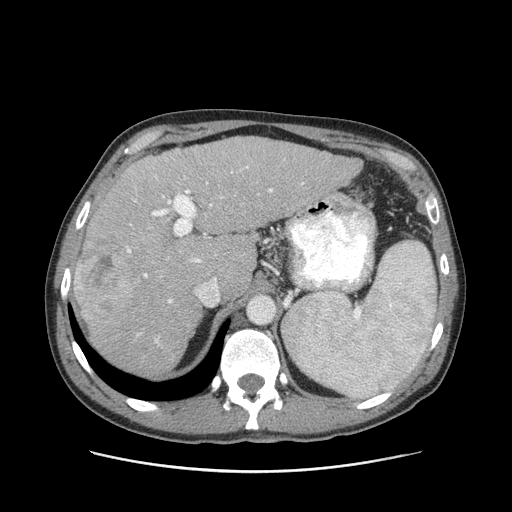
Contrast-enhanced abdominal CT (liver protocol), one axial slice. Slice 67 of 93 in the series (ordered by position). Soft-tissue window (W 400 / L 40 HU). 2.5 mm slice thickness. 512 × 512 image matrix. Case-level facts recorded for this patient, not image findings: diagnosis: hepatocellular carcinoma (patient treated with transarterial chemoembolisation; whether this scan precedes or follows treatment is not stated here); TNM stage (as recorded): Stage-II; Child-Pugh class: A; tumour differentiation: moderately differentiated; tumour nodularity: multinodular.
Annotated regions visible in this slice (semi-automatically segmented with operator editing):
- liver parenchyma outside the tumour (the mass and vessels are separate outlines, so this box may not span the whole liver): bounding box (x1, y1, x2, y2) in pixels: (72, 136, 360, 376)
- mass: (76, 238, 137, 317)
- liver vessels: (127, 166, 304, 344)